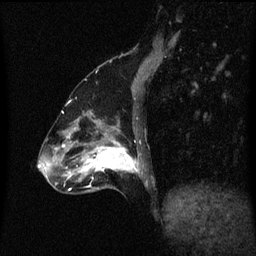
Breast MRI (dynamic contrast-enhanced), one sagittal slice. Position 21 of 60 along the scan axis. Dynamic contrast-enhanced series, image 2 of 3 at this slice position (ordered by acquisition). 1.5 T. TE 4.2 ms, TR 8.4 ms. 2 mm slice thickness. 256 × 256 image matrix, field of view 200 × 200 mm. Female patient, age 47 years.
Structures marked on this image (semi-automatic segmentation, software-assisted and operator-edited):
- analysis volume of interest (the breast-tissue region the enhancement analysis was run in; not a lesion): bounding box (x1, y1, x2, y2) in pixels: (85, 136, 142, 193)
- tumour enhancement mask (voxels above the 70 % enhancement threshold inside the analysis volume of interest): (85, 140, 140, 179)